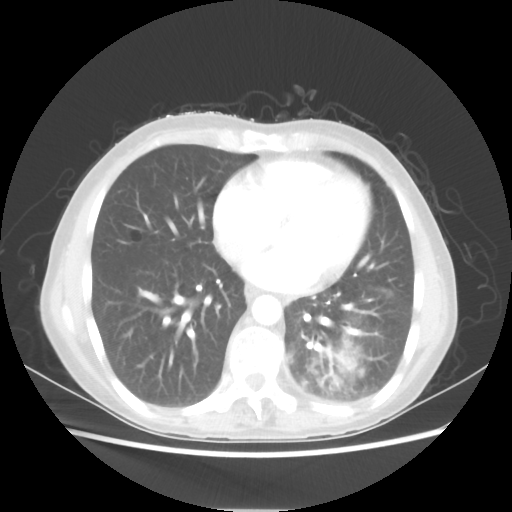
Chest CT, one axial slice. Reconstruction kernel STANDARD. 80 kVp. Lung window (W 1500 / L -600 HU). 5 mm slice thickness. 512 × 512 image matrix, field of view 360 × 360 mm. Female patient, age 53 years. From the clinical record (not read from this slice): clinical TNM (as recorded): T3 N0 M0.
Outlined on this slice (rectangle marked by the reading radiologist):
- lung tumour (recorded histology: adenocarcinoma): bounding box <319,335,358,389> (left, top, right, bottom; pixels)